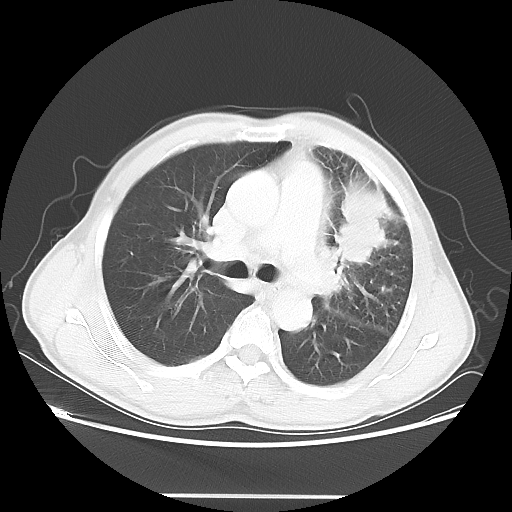
Chest CT, one axial slice; slice 33 of 55 in the series (ordered by position); reconstruction kernel LUNG; 100 kVp; lung window (W 1500 / L -600 HU); 5 mm slice thickness; 512 × 512 image matrix, field of view 398 × 398 mm. Male patient, age 60 years. Case-level facts recorded for this patient, not image findings: clinical TNM (as recorded): T3 N3 M0.
Outlined on this slice (rectangle marked by the reading radiologist):
- lung tumour (recorded histology: adenocarcinoma): bounding box (x1, y1, x2, y2) in pixels: (333, 181, 395, 274)